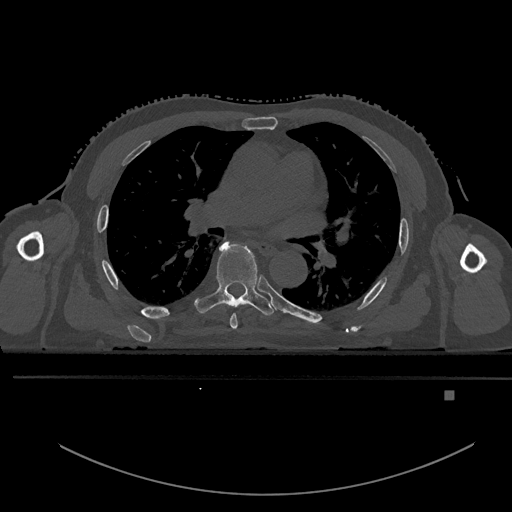
CT including the spine, one axial slice; position 319 of 969 along the scan axis; bone window (W 1800 / L 400 HU); 0.5 mm slice thickness; 512 × 512 image matrix, field of view 456 × 456 mm. Patient: male, 82 years. Case-level facts recorded for this patient, not image findings: primary cancer: prostate.
Structures marked on this image (semi-automatic segmentation, software-assisted and operator-edited):
- T5 vertebra: bounding box (x1, y1, x2, y2) in pixels: (230, 313, 238, 329)
- T6 vertebra: (194, 239, 275, 316)